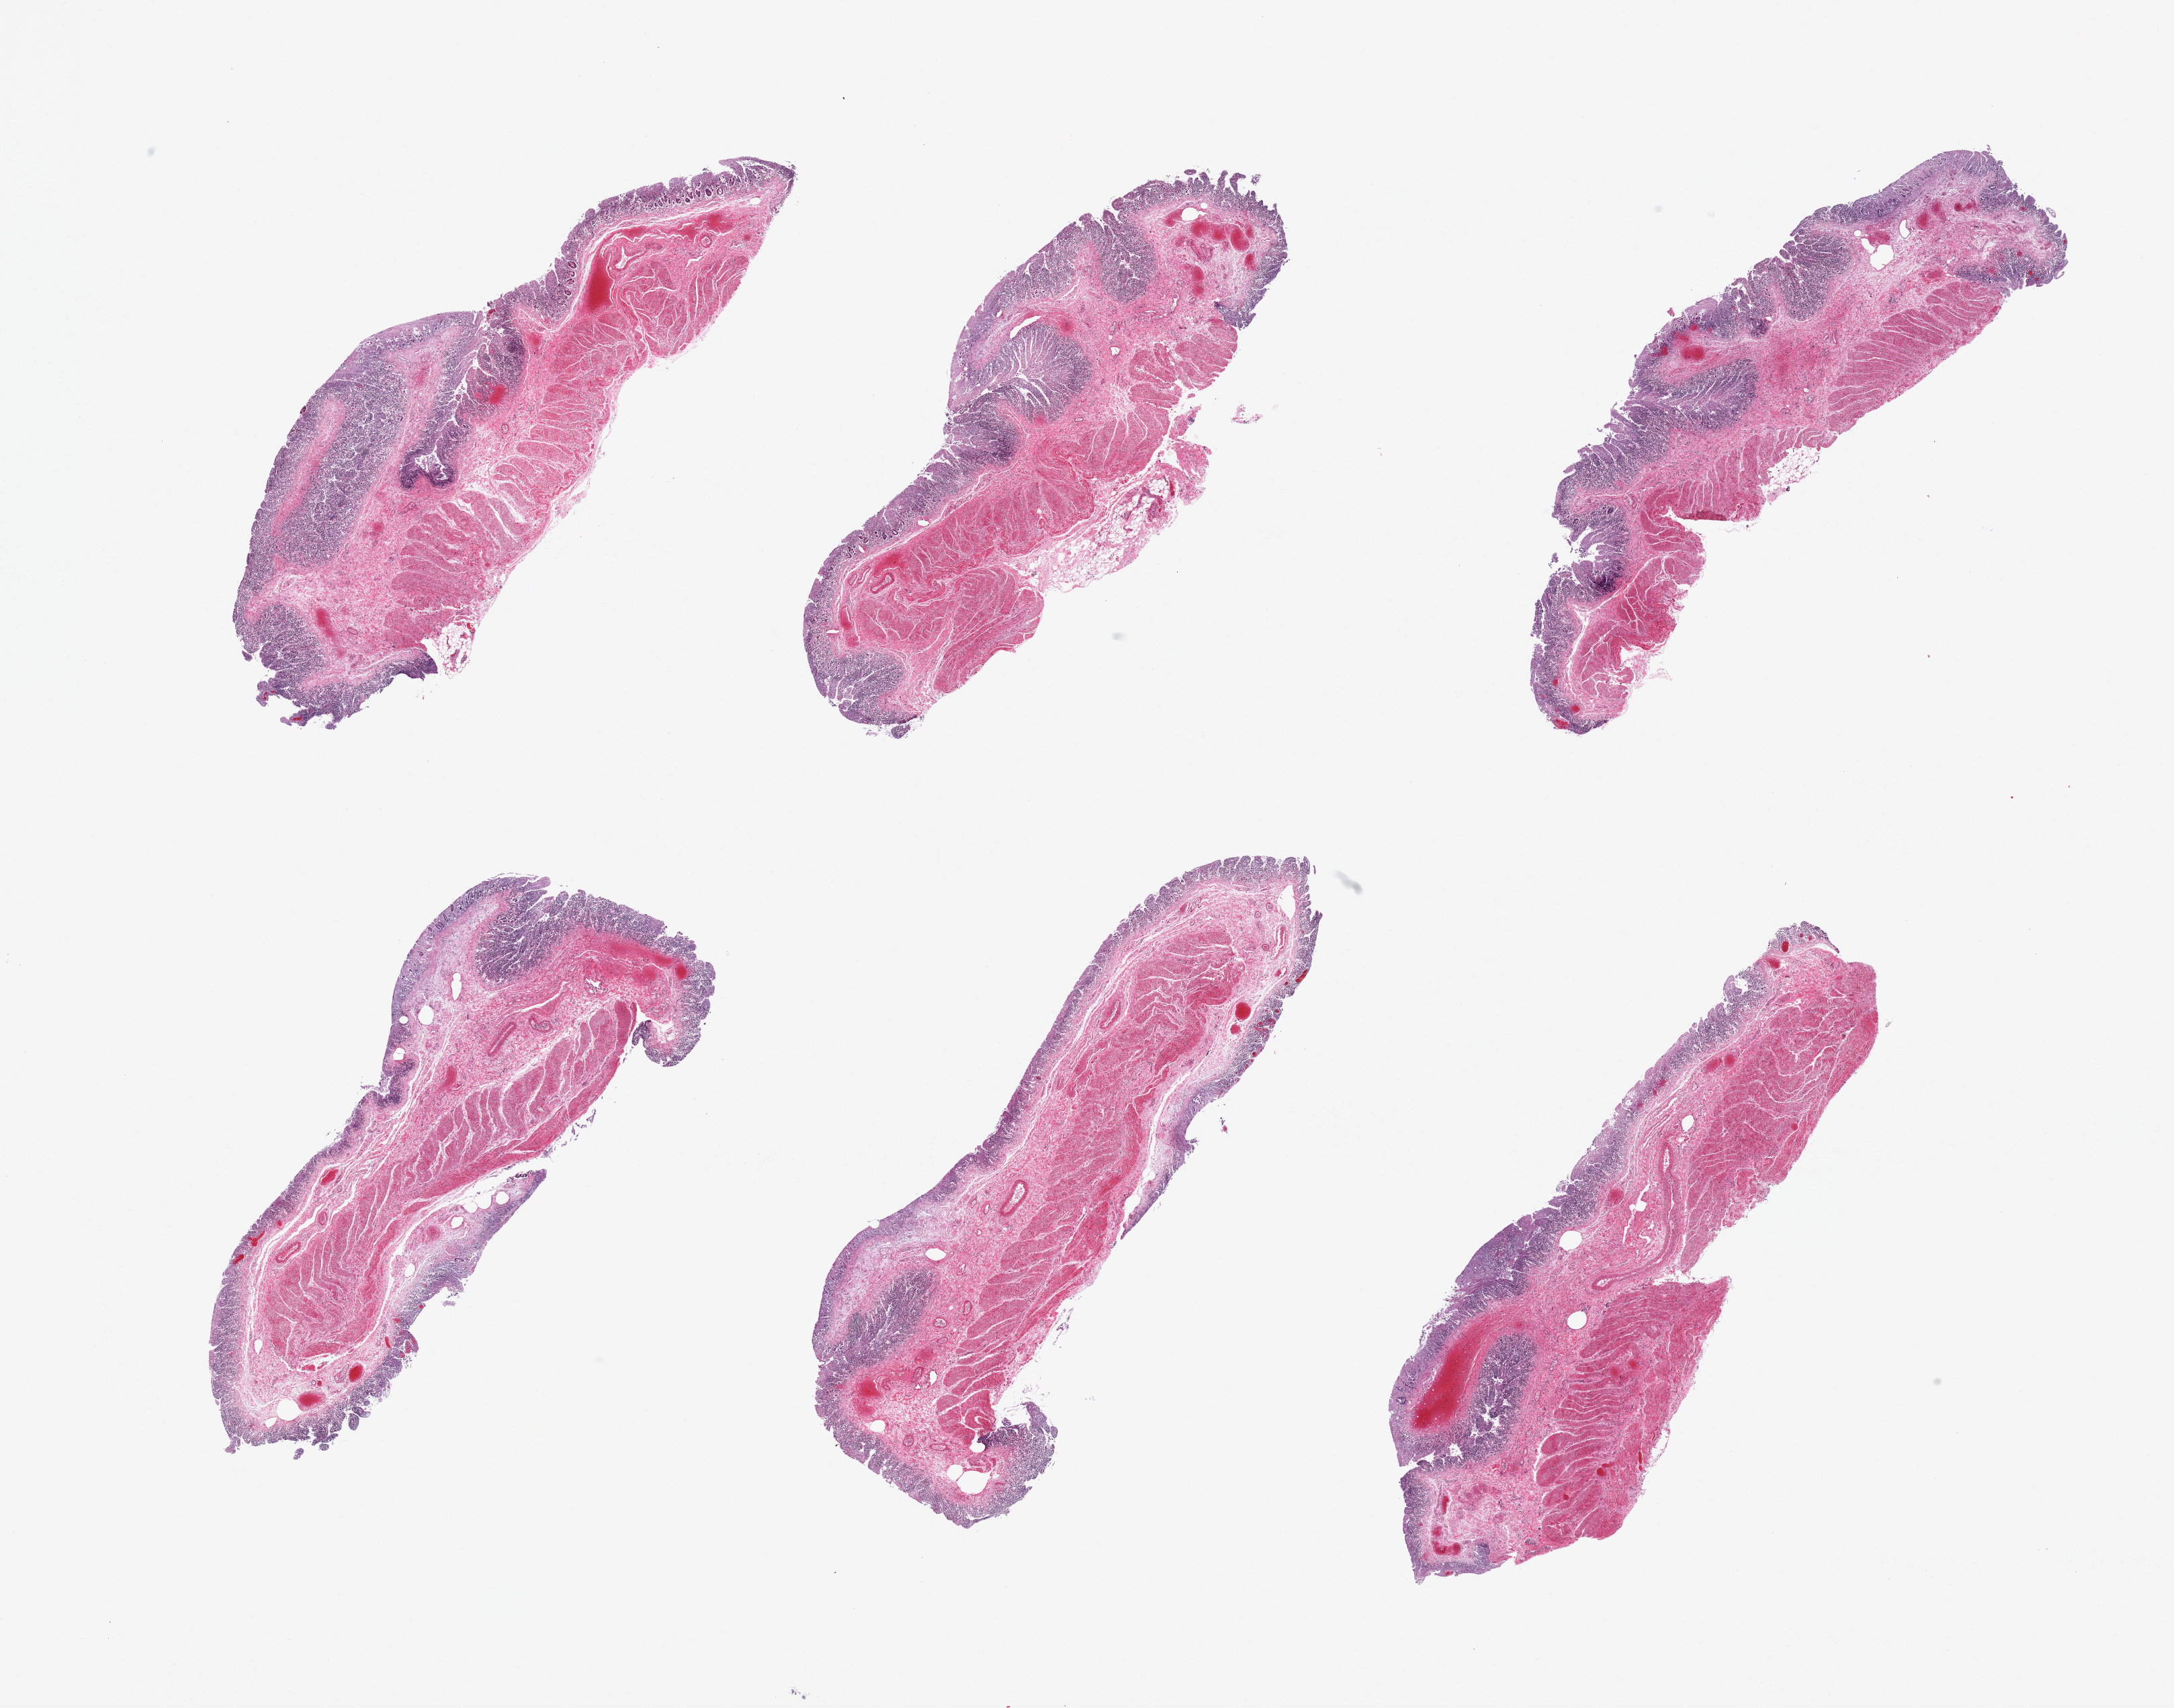
Digitized H&E-stained section, brightfield — a low-resolution overview of the entire scanned area, about 25.6 x 20.1 mm (from a 20x scan); PAXgene-fixed paraffin-embedded (PFPE) section; section of transverse colon (target tissue); tissue donor sample. Donor sex: female.
Pathologist's review note for this sample: 6 pieces, target mucosa up to ~0.5mm, lamina propria only, glandular elements completely autolyzed/sloughed.